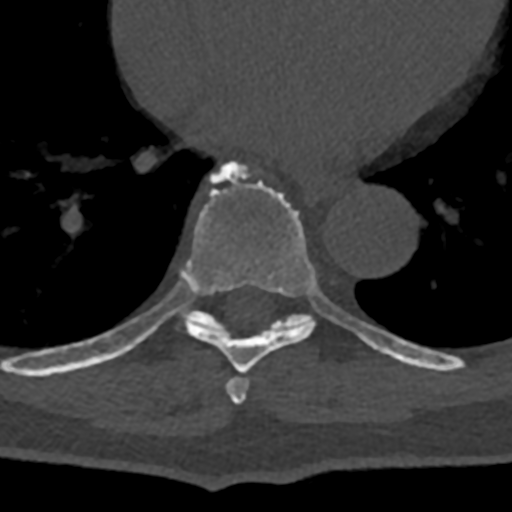
CT including the spine, one axial slice; slice 696 of 797 in the series (ordered by position); bone window (W 1800 / L 400 HU); 0.5 mm slice thickness; 512 × 512 image matrix, field of view 160 × 160 mm. Patient: male, 74 years. Case-level facts recorded for this patient, not image findings: primary cancer: renal.
Annotated regions visible in this slice (semi-automatic segmentation, software-assisted and operator-edited):
- T7 vertebra: box from (x=226, y=377) to (x=249, y=404) px
- T8 vertebra: (x=70, y=160)–(x=400, y=374)
- T9 vertebra: (x=169, y=279)–(x=432, y=369)